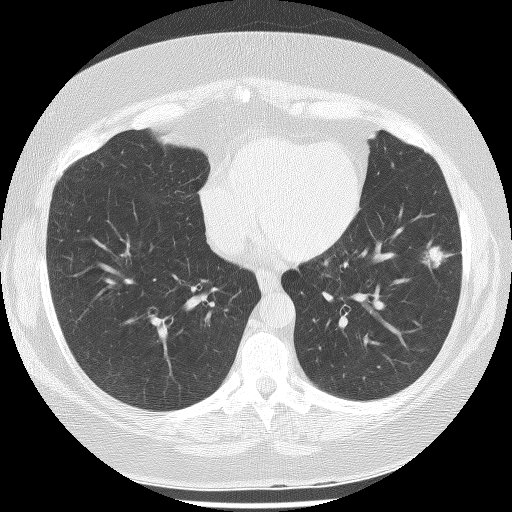
Axial slice from a low-dose chest CT screening exam. First (baseline) screen. Lung window (W 1500 / L -600 HU). Lung (sharp) reconstruction kernel (BONE). Slice 134 of 233 in the series. 512 × 512 image matrix, field of view 340 × 340 mm. Female, age 56 years at enrolment. Former smoker at enrolment.
Expert reader's lesion annotation, bounding box <391,225,464,286> (left, top, right, bottom; pixels). The exam's reader record, not a measurement of the box and not confirmed to be the same lesion: non-calcified nodule or mass ≥4 mm, left lower lobe, 22 × 17 mm, spiculated (stellate) margins, soft tissue attenuation. Official screen result: positive, change unspecified: nodule(s) >= 4 mm or enlarging nodule(s), mass(es), or other non-specific abnormalities suspicious for lung cancer. Lung cancer was diagnosed 63 days after this screen: bronchiolo-alveolar adenocarcinoma, NOS, left lower lobe, stage IA (AJCC 6th edition), 18 mm at pathology.